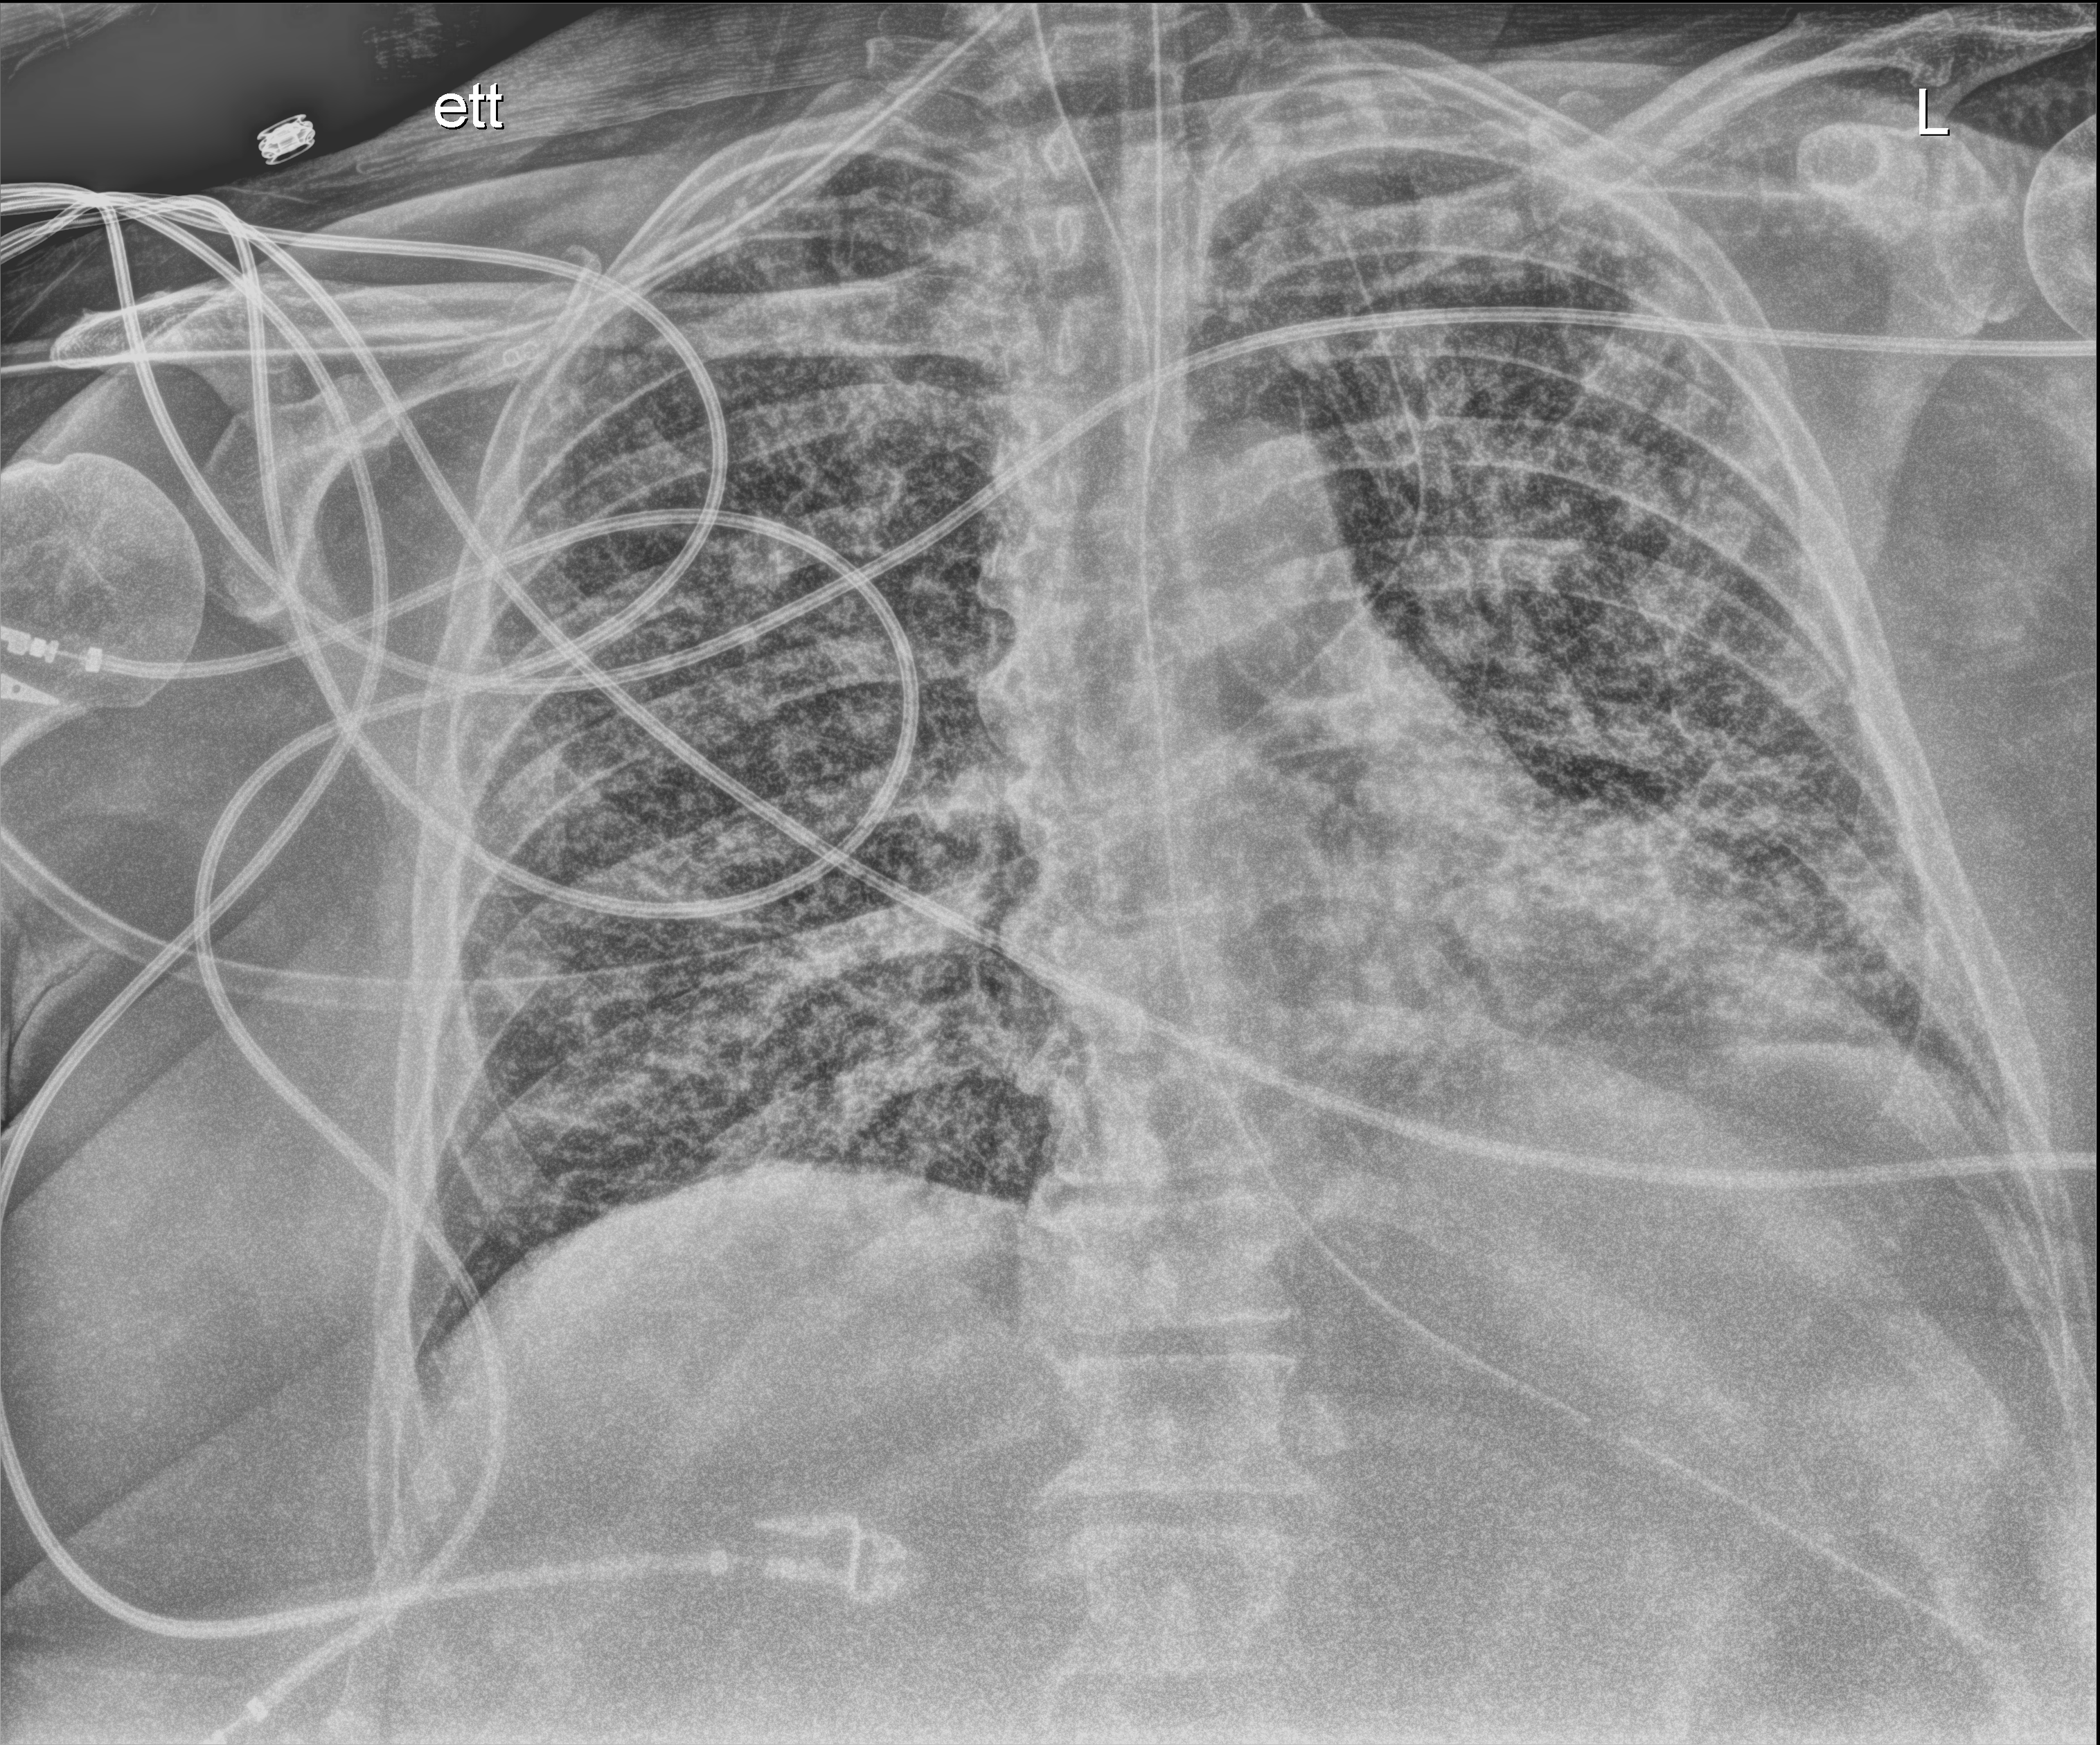
Chest X-ray (portable); anteroposterior (AP) projection. Adult patient hospitalised with COVID-19, age 18–59 years.
Hospital-stay facts (about this admission, not read from this image; timing relative to this image not recorded):
- length of hospital stay: 28 days
- mechanically ventilated during this hospital stay: yes